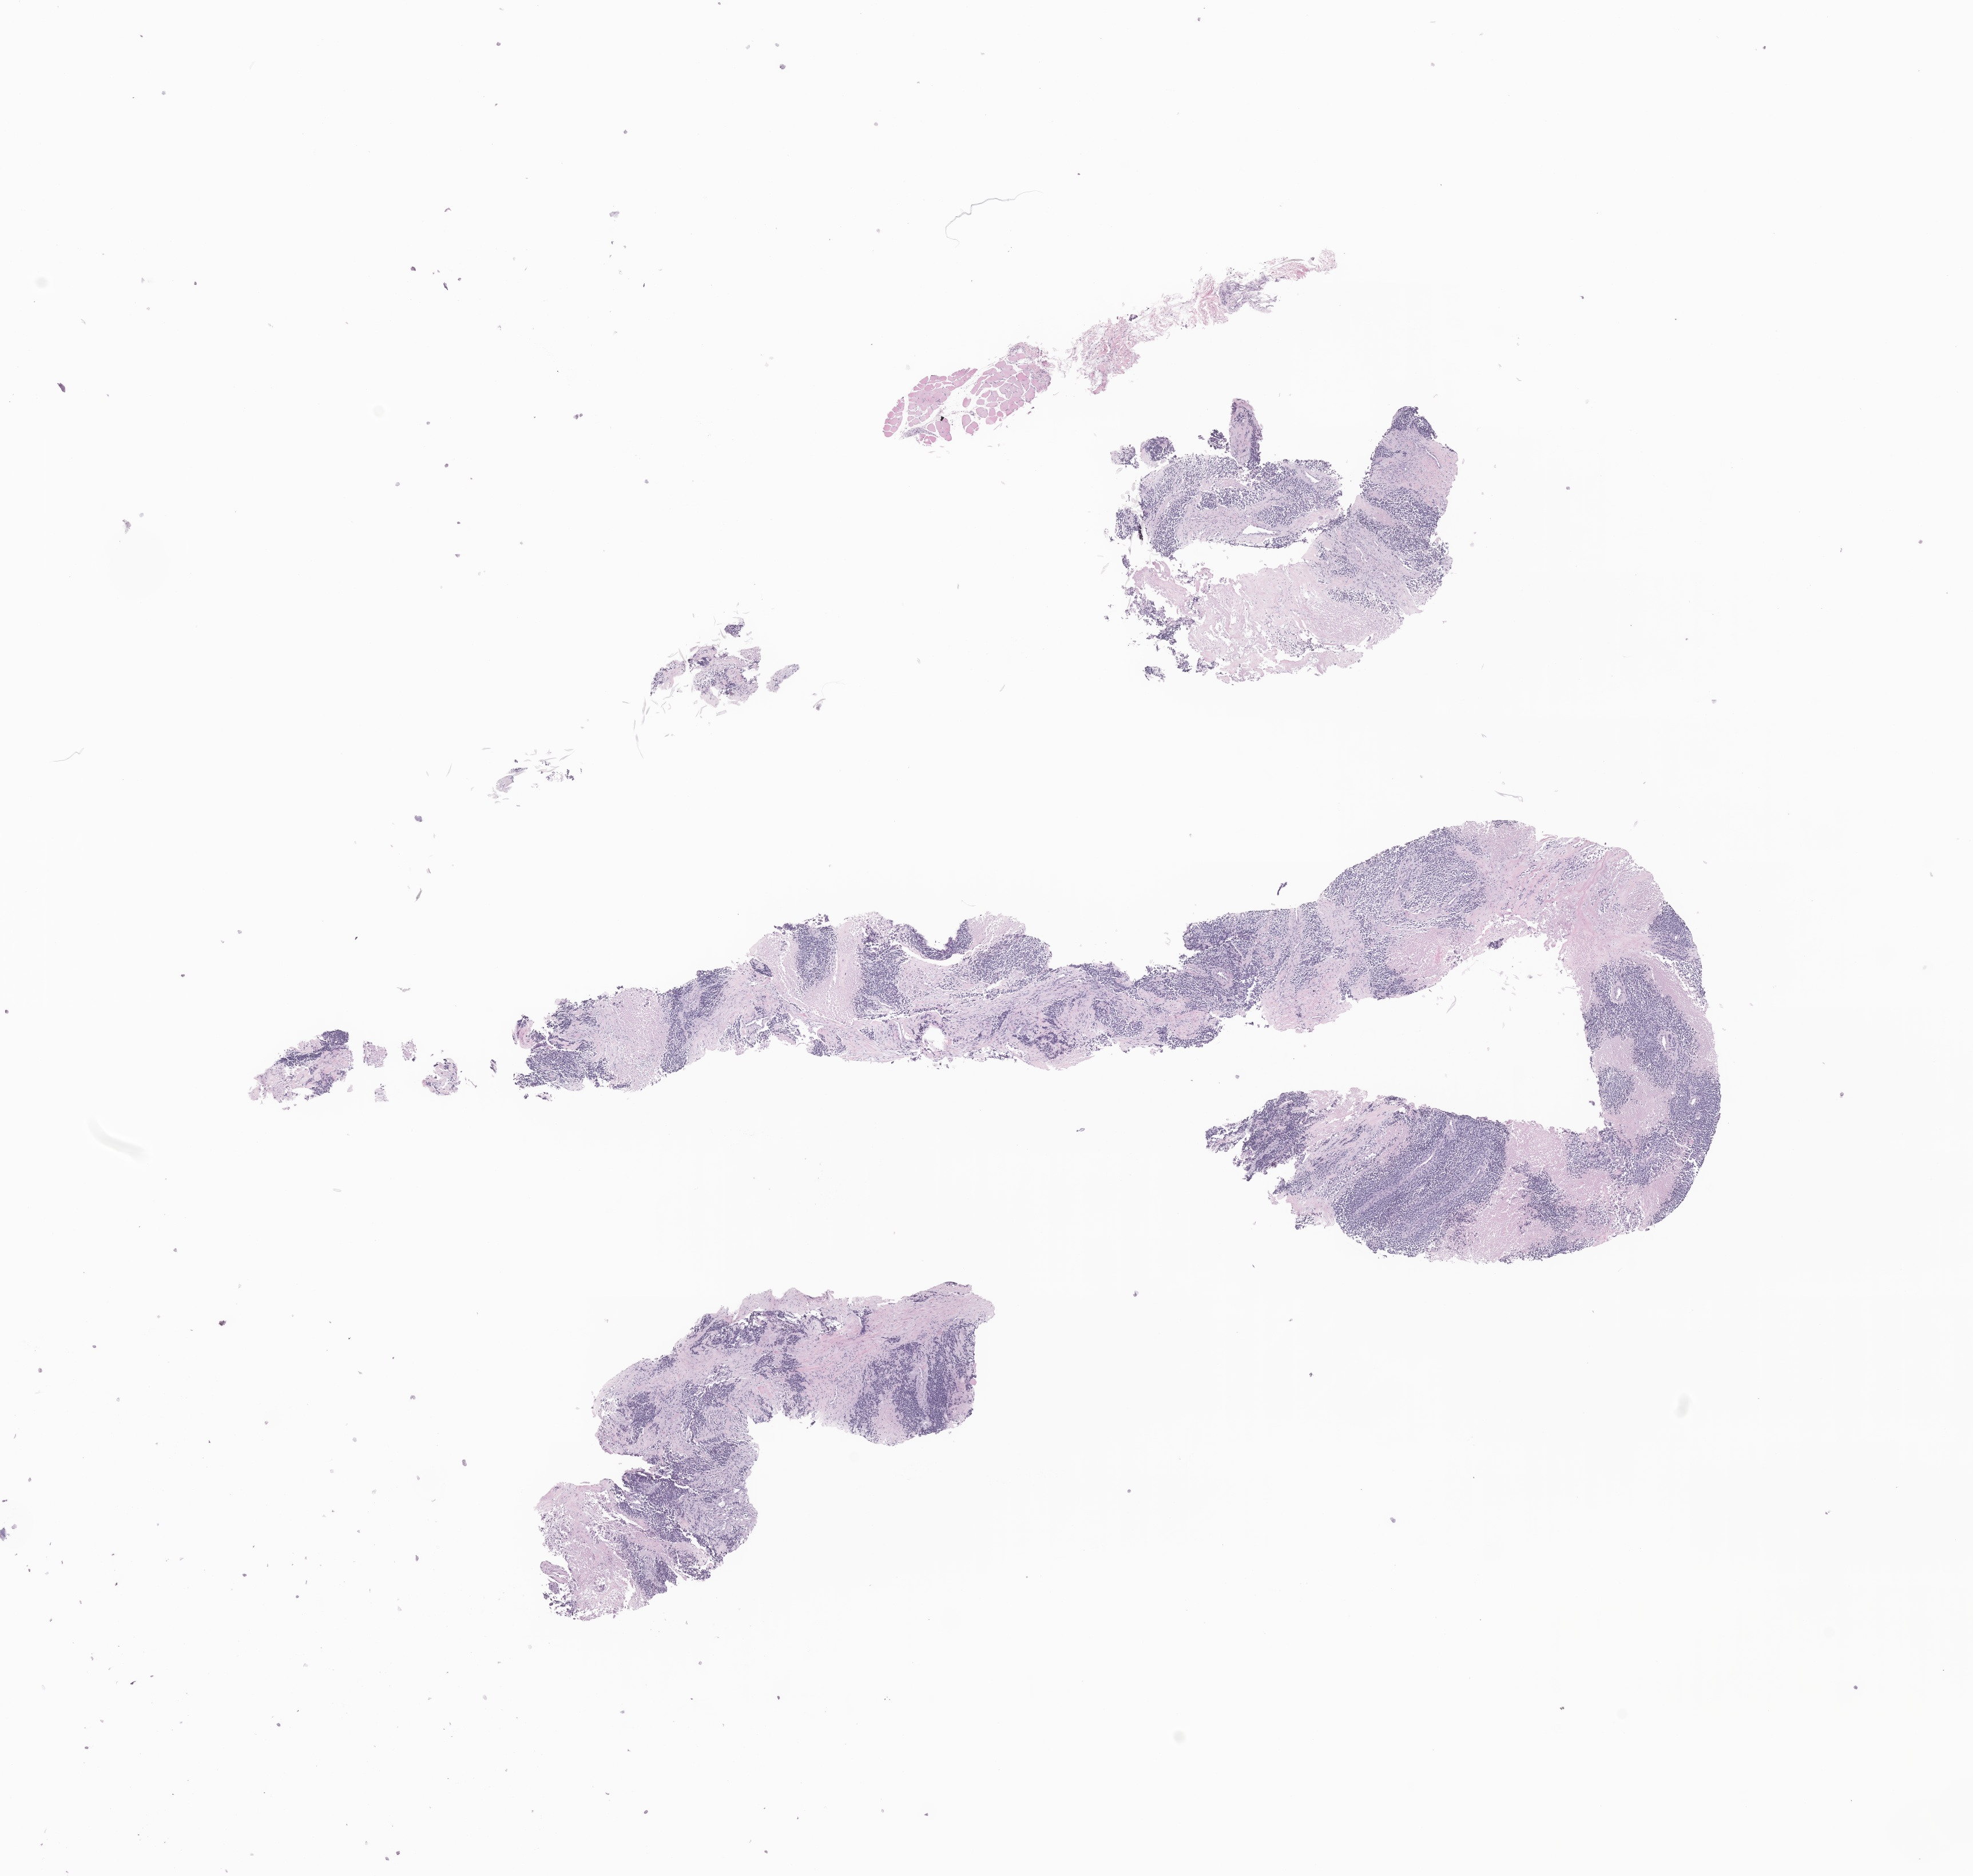
Whole-slide image, haematoxylin and eosin stain of tumor tissue from the upper limb lymph node, low-resolution overview of the scanned area, about 14.5 x 13.8 mm. Formalin-fixed paraffin-embedded section. Patient: female, age 192 months (16 years).
• recorded diagnosis: Rhabdomyosarcoma, NOS